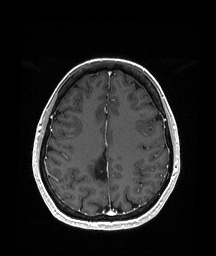
Brain MRI from a brain-tumour surgery series, one axial slice. Position 69 of 151 along the scan axis. T1-weighted post-contrast. 216 × 256 image matrix. From the clinical record (not read from this slice): histopathology: Oligodendroglioma; WHO grade: 2; IDH mutation: yes.
Structures marked on this image (expert manual segmentation):
- previous resection cavity: bounding box <94,149,109,183> (left, top, right, bottom; pixels)